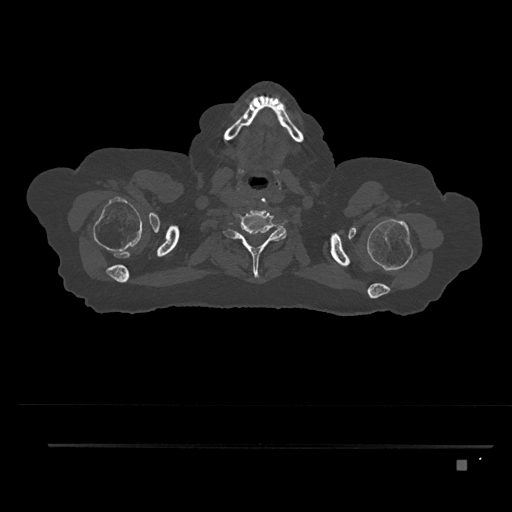
CT including the spine, one axial slice; slice 733 of 797 in the series (ordered by position); bone window (W 1800 / L 400 HU); 0.5 mm slice thickness; 512 × 512 image matrix, field of view 437 × 437 mm. Patient: female, 76 years. Case-level facts recorded for this patient, not image findings: primary cancer: lung; vertebrae with lytic lesions (as recorded): T11, L3.
Annotated regions visible in this slice (semi-automatic segmentation, software-assisted and operator-edited):
- T1 vertebra: box from (x=244, y=245) to (x=252, y=254) px